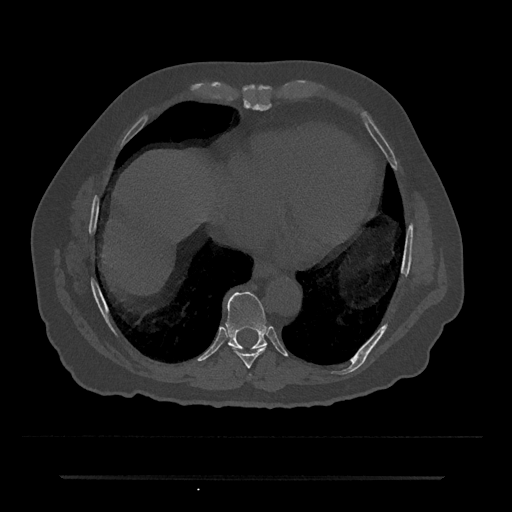
CT including the spine, one axial slice. Slice 305 of 797 in the series (ordered by position). 120 kVp. Bone window (W 1800 / L 400 HU). 0.5 mm slice thickness. 512 × 512 image matrix, field of view 437 × 437 mm. Male patient, age 69 years. From the clinical record (not read from this slice): primary cancer: prostate.
Outlined on this slice (semi-automatically segmented with operator editing):
- T8 vertebra: bounding box <230,346,267,368> (left, top, right, bottom; pixels)
- T9 vertebra: <226,291,267,350>